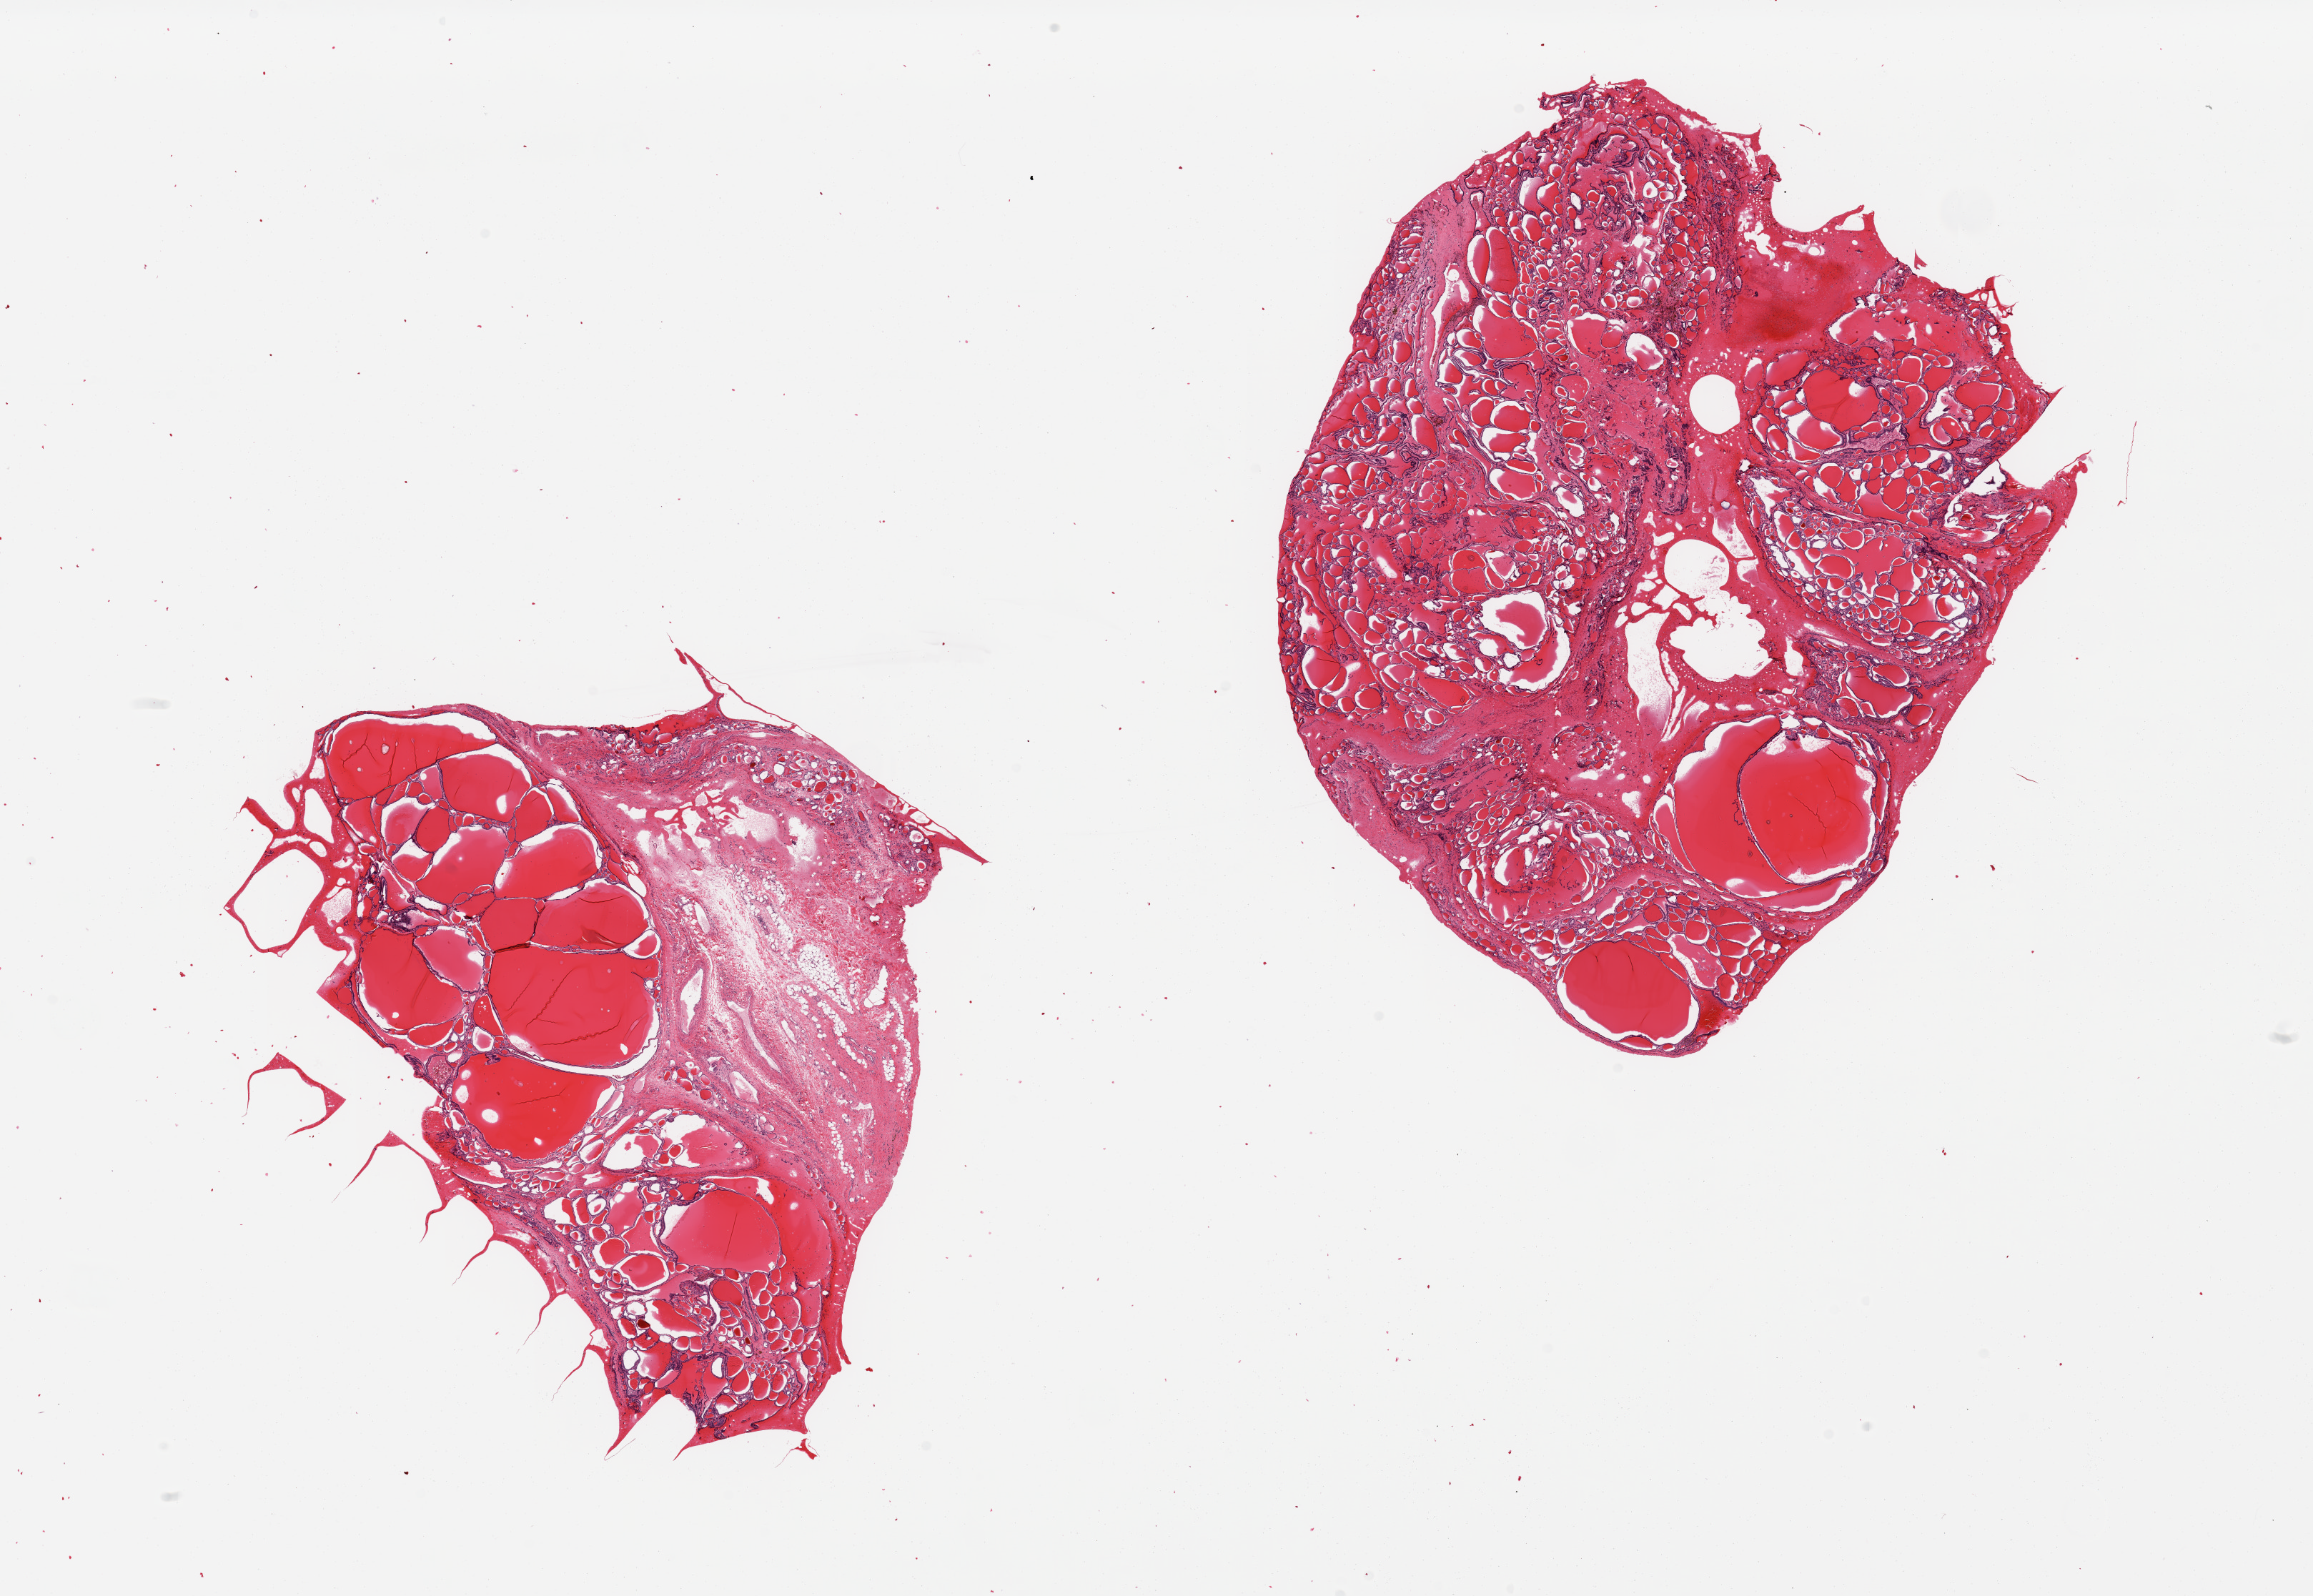
Digitized hematoxylin and eosin (H&E)-stained section, low-resolution overview of the scanned area, about 25.6 x 17.7 mm; PAXgene-fixed, paraffin-embedded tissue; sampled site (target tissue): thyroid; tissue donor sample. Female donor.
• reviewer comment on this tissue sample: 2 pieces, multinodular goiter, colloid nodules up to ~5mm